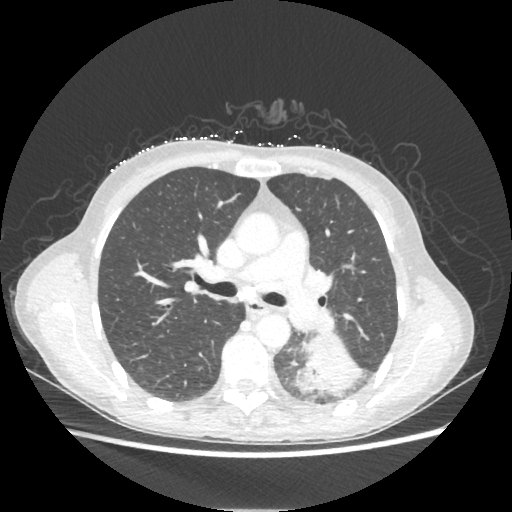
Chest CT, one axial slice. Position 134 of 221 along the scan axis. Reconstruction kernel STANDARD. 80 kVp. Lung window (W 1500 / L -600 HU). 1.25 mm slice thickness. 512 × 512 image matrix. Patient: female, 53 years. Case-level facts recorded for this patient, not image findings: clinical TNM (as recorded): T3 N0 M0.
Annotated regions visible in this slice (rectangle marked by the reading radiologist):
- lung tumour (recorded histology: adenocarcinoma): bounding box (x1, y1, x2, y2) in pixels: (295, 332, 361, 396)